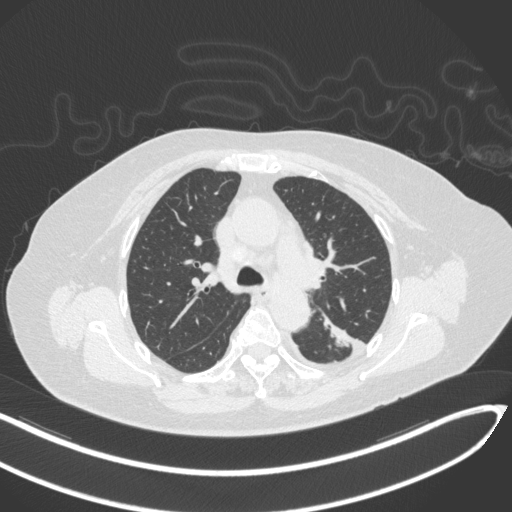
Chest CT, one axial slice. Position 213 of 270 along the scan axis. Lung window (W 1500 / L -600 HU). 512 × 512 image matrix. Female patient, age 76 years. From the clinical record (not read from this slice): clinical TNM (as recorded): T1c N0 M0.
Outlined on this slice (rectangle marked by the reading radiologist):
- lung tumour (recorded histology: adenocarcinoma): bounding box [x1, y1, x2, y2] px = [316, 303, 354, 347]